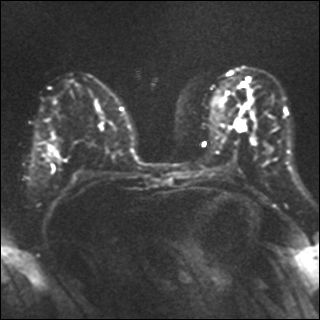
Breast MRI, one axial slice. Position 18 of 40 along the scan axis. Diffusion-weighted series; image 2 of 4 stored at this slice position (different b-values; order by instance number). 1.5 T. 4 mm slice thickness. 320 × 320 image matrix, field of view 320 × 320 mm. Female patient.
Outlined on this slice (expert manual segmentation):
- tumour on diffusion-weighted imaging: bounding box (x1, y1, x2, y2) in pixels: (234, 117, 248, 132)